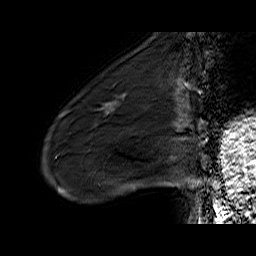
Breast MRI (dynamic contrast-enhanced), one sagittal slice; slice 16 of 60 in the series (ordered by position); dynamic contrast-enhanced series, time point 2 of 6 at this slice position (early post-contrast); 1.5 T; TE 6.5 ms, TR 32.9 ms; 4 mm slice thickness; 256 × 256 image matrix, field of view 200 × 200 mm. Female patient. Case-level facts recorded for this patient, not image findings: setting: breast cancer imaged before/during neoadjuvant chemotherapy; receptor status: HER2-positive.
Annotated regions visible in this slice (semi-automatic segmentation, software-assisted and operator-edited):
- analysis volume of interest (the breast-tissue region the enhancement analysis was run in; not a lesion): bounding box <72,88,133,137> (left, top, right, bottom; pixels)
- tumour enhancement mask (voxels above the 100 % enhancement threshold inside the analysis volume of interest): <122,95,125,97>